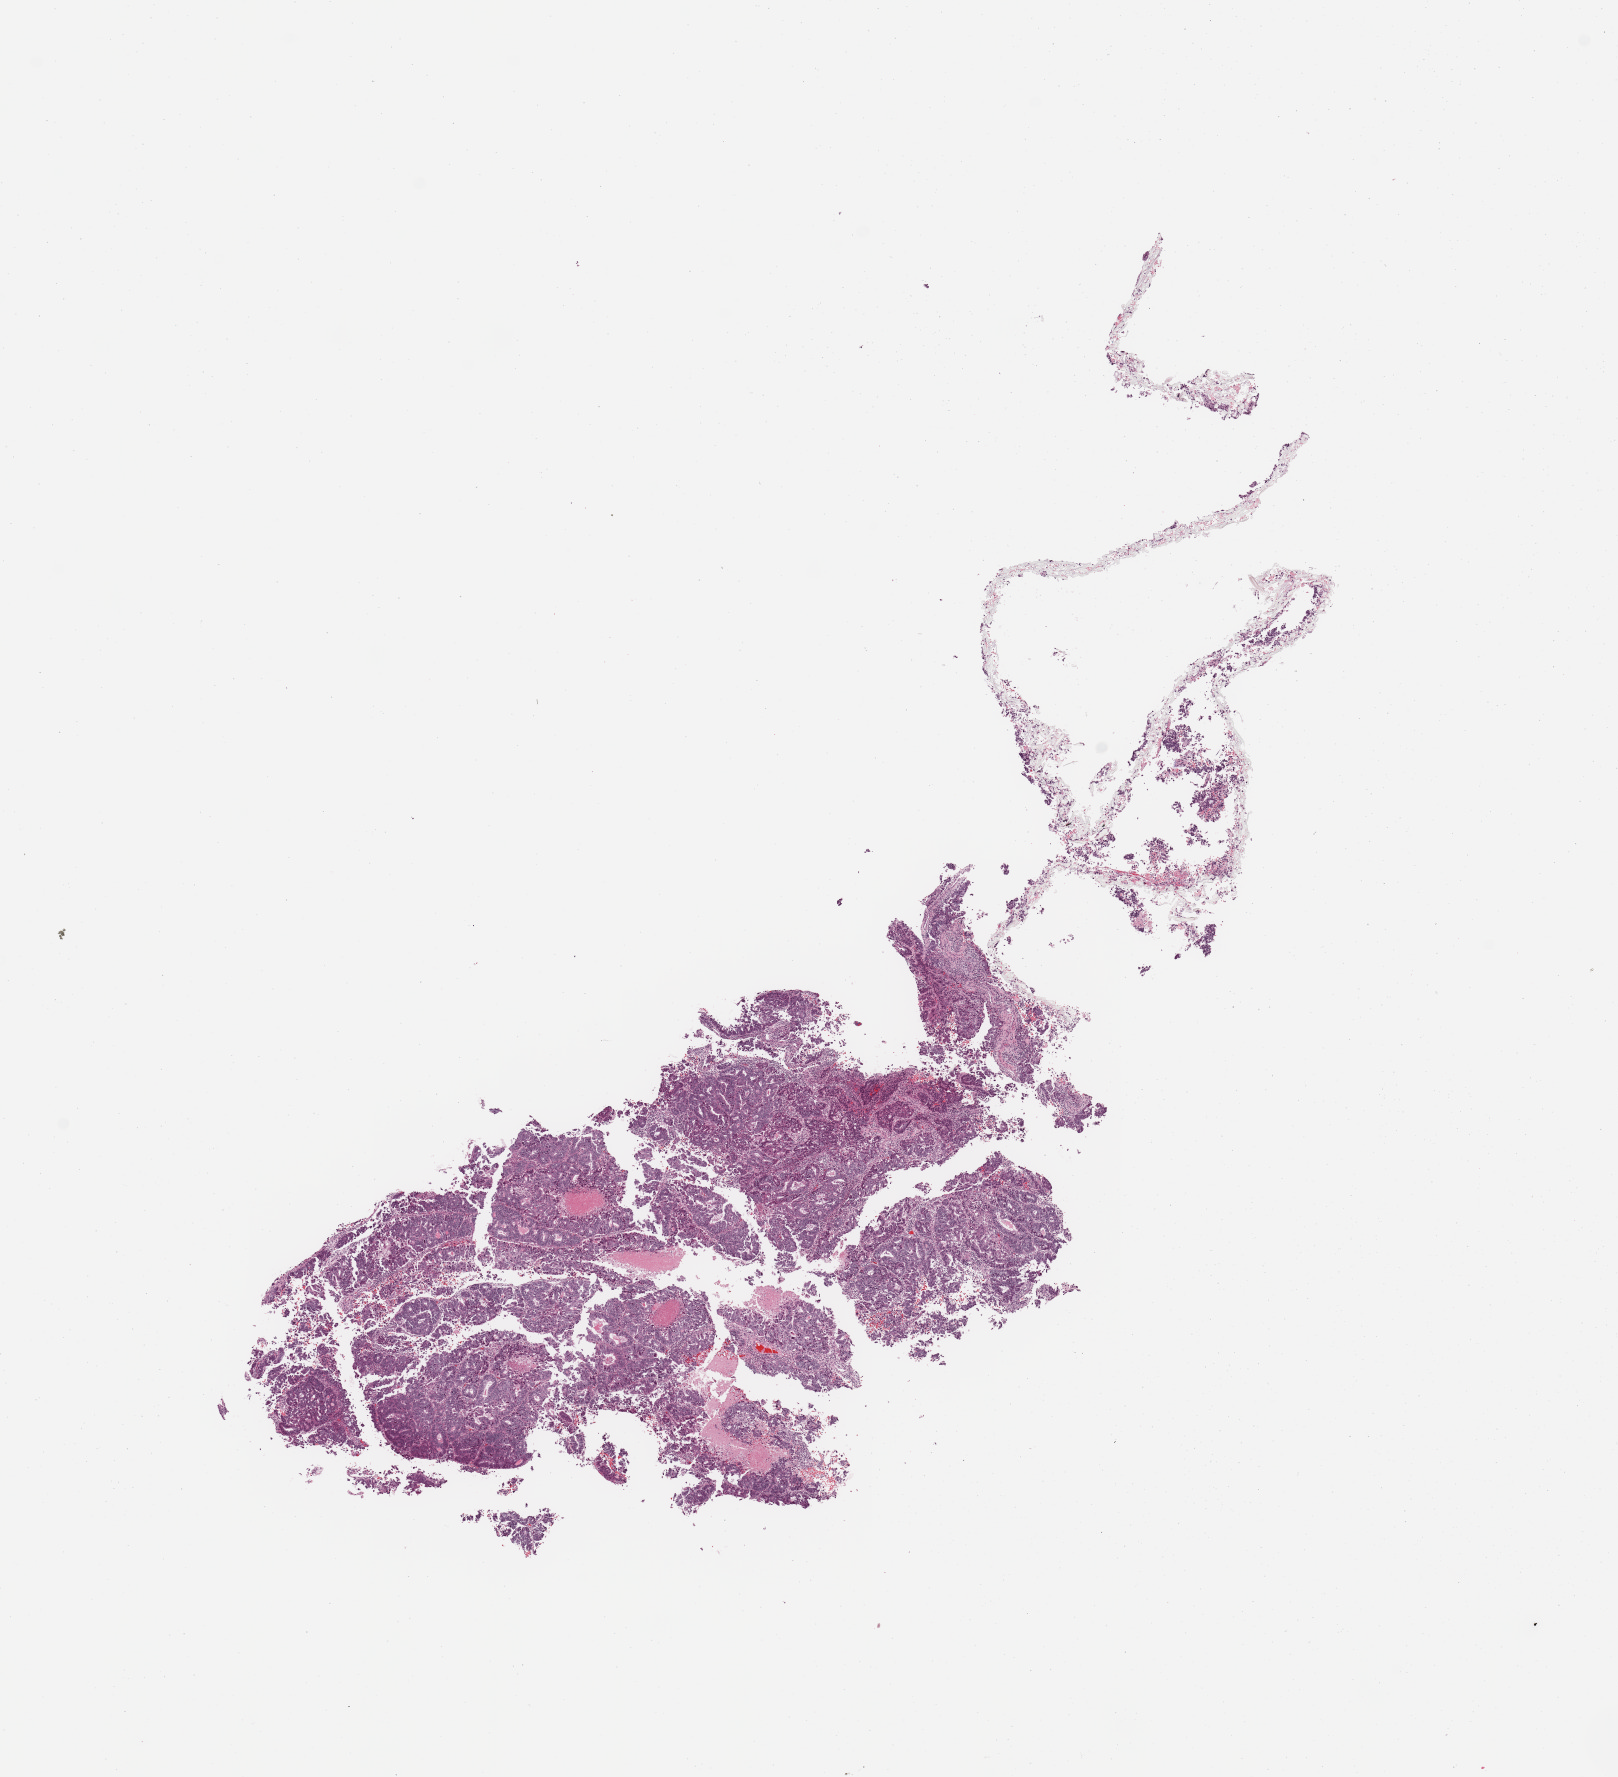
Hematoxylin and eosin (H&E) stained whole-slide image, a low-resolution overview of the entire scanned area, about 12.8 x 14.1 mm (acquisition: 20x scan). Uterus, tissue type not recorded.
• patient diagnosis (cohort enrolment): corpus endometrial carcinoma (uterus)